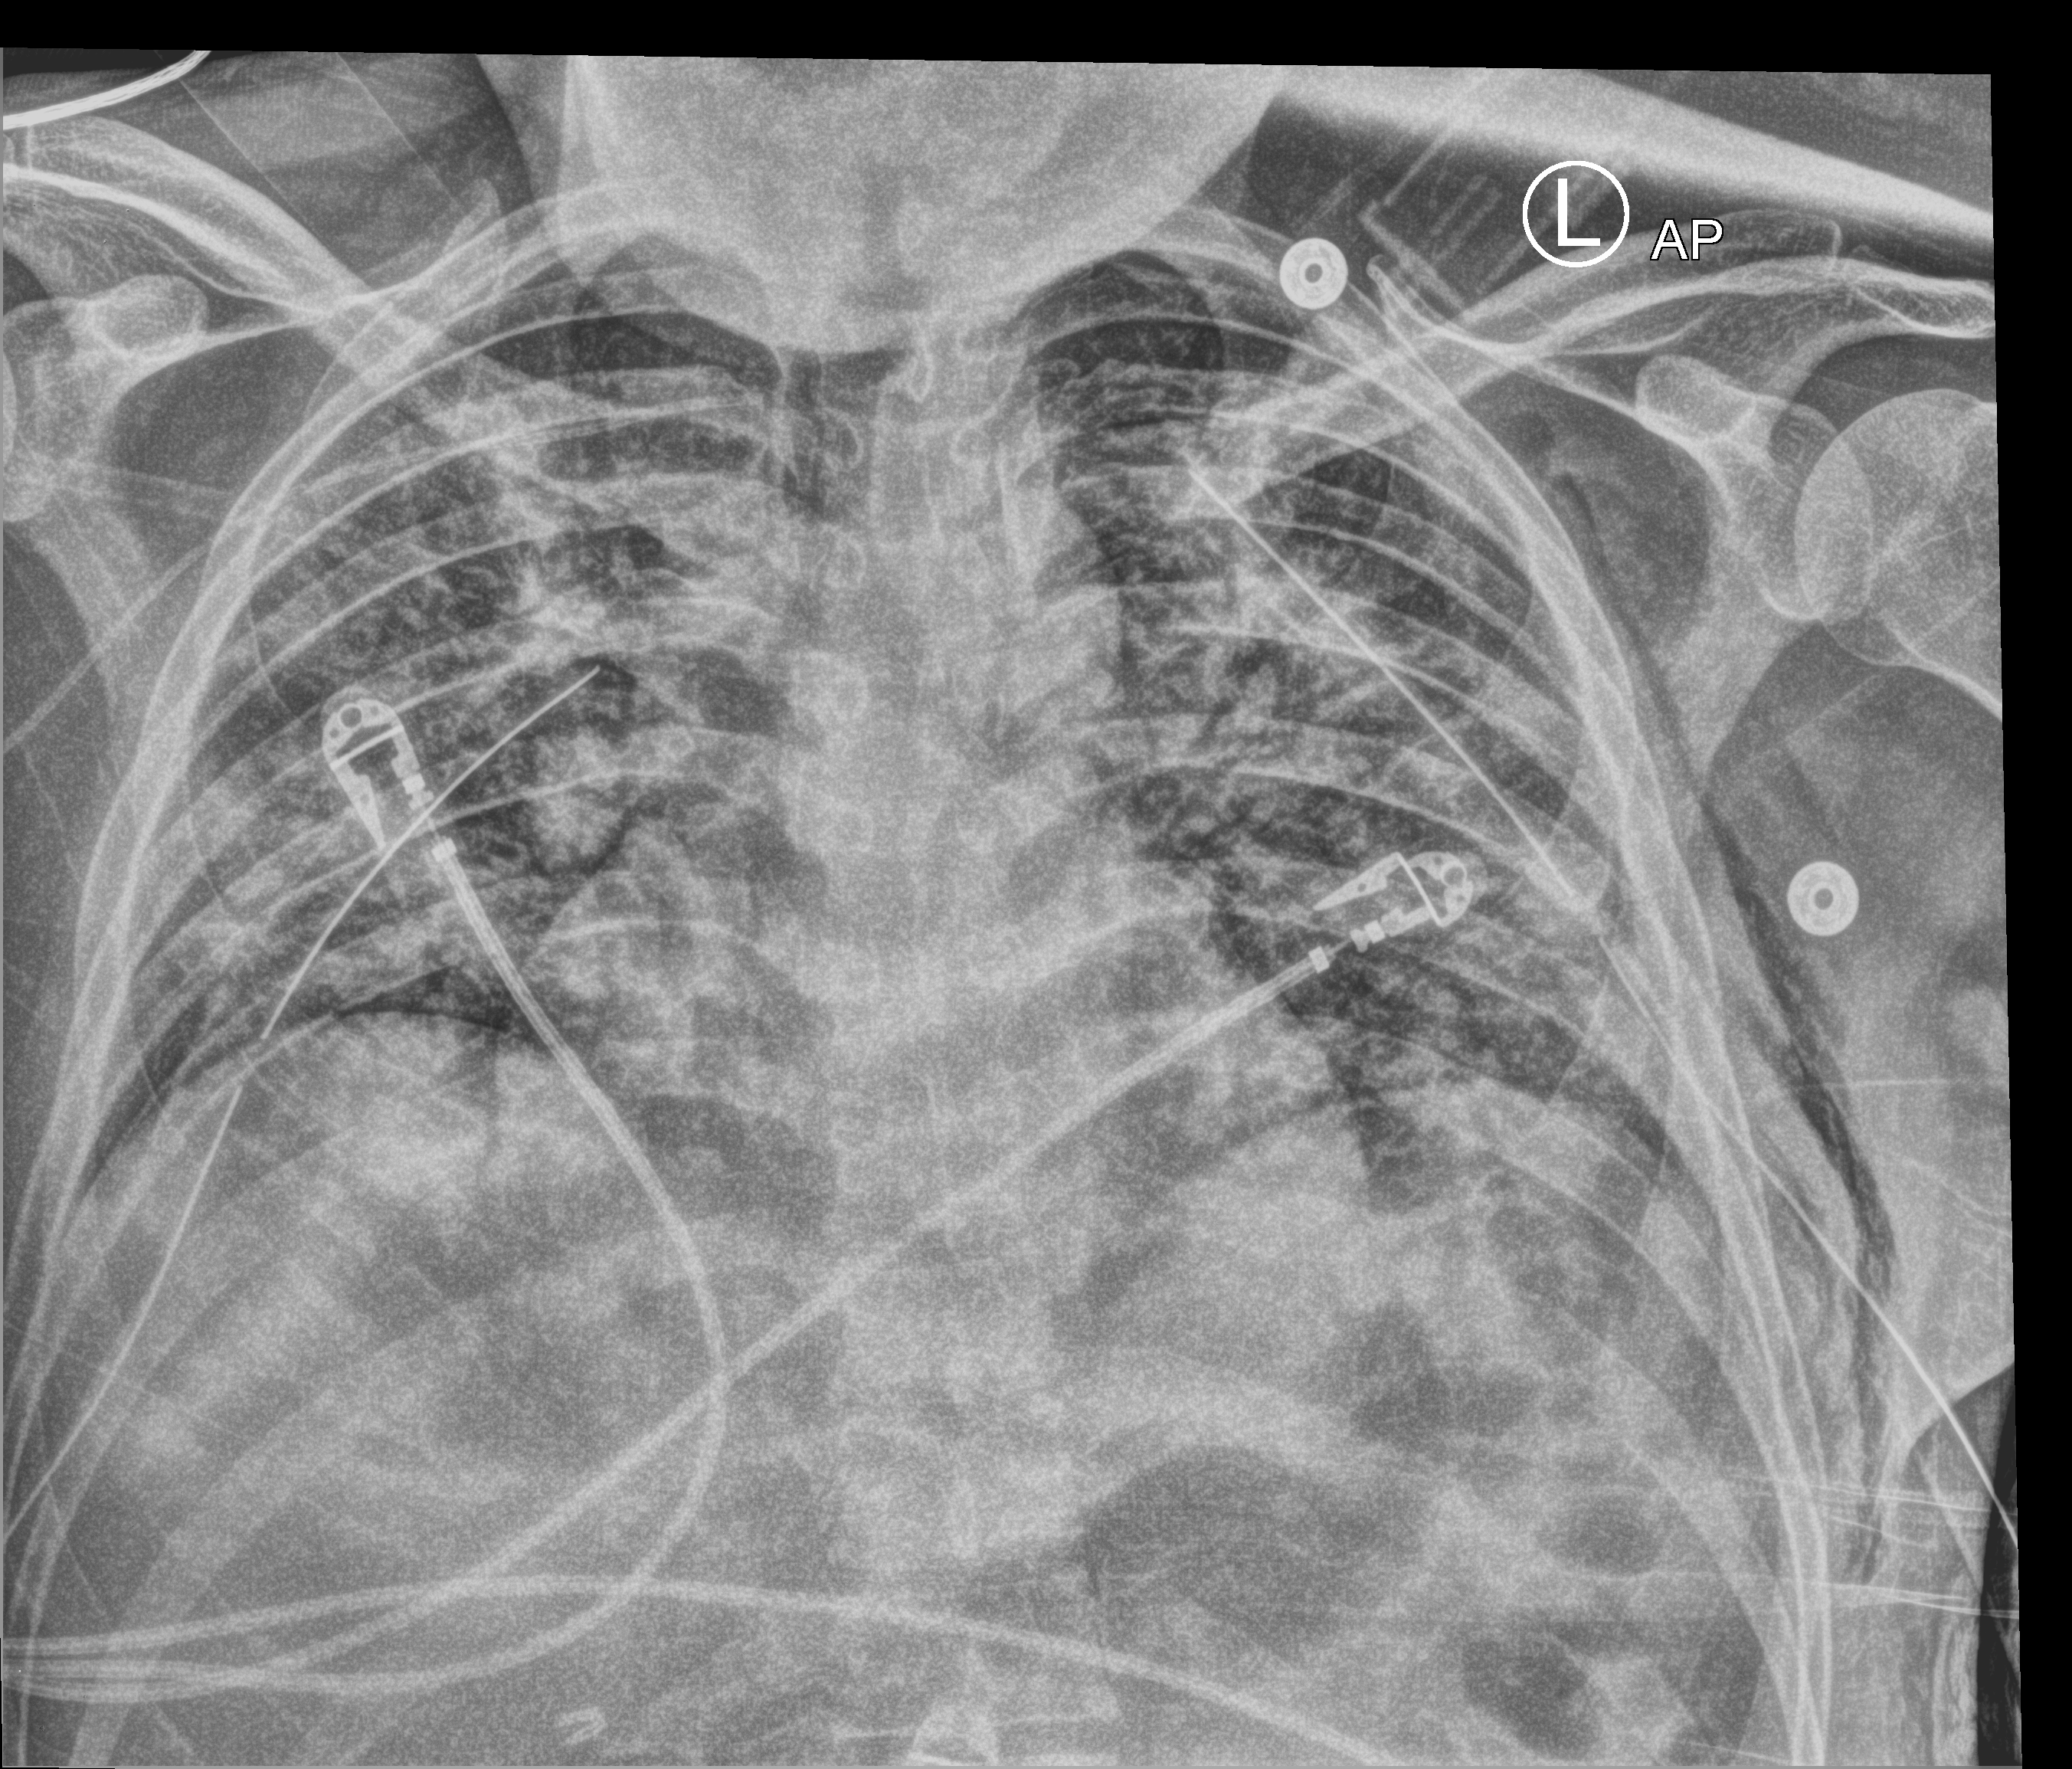
Chest X-ray (portable); anteroposterior (AP) projection. Patient hospitalised with COVID-19; male, aged 18–59 years.
From the hospital-stay record, not from the radiograph (when in the stay this image was taken is not recorded):
- mechanically ventilated during this hospital stay: yes